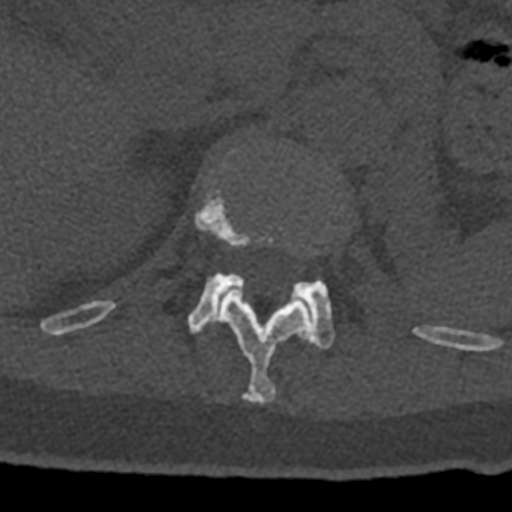
CT including the spine, one axial slice. Reconstruction kernel Br40s/3. 120 kVp. Bone window (W 1800 / L 400 HU). 512 × 512 image matrix, field of view 160 × 160 mm. Patient: male, 74 years. Case-level facts recorded for this patient, not image findings: primary cancer: renal; vertebrae with lytic lesions (as recorded): T10, L1, L2, L3, L4, L5.
Outlined on this slice (semi-automatic segmentation, software-assisted and operator-edited):
- L1 vertebra: bounding box [x1, y1, x2, y2] px = [187, 273, 335, 349]
- T12 vertebra: [70, 163, 432, 403]